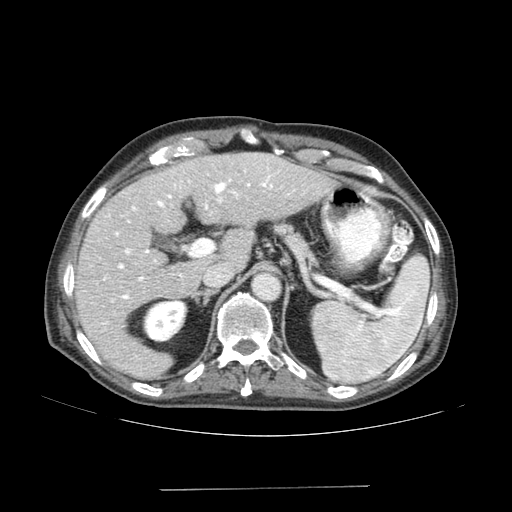
Contrast-enhanced abdominal CT (liver protocol), one axial slice; position 106 of 192 along the scan axis; reconstruction kernel SOFT; 120 kVp; soft-tissue window (W 400 / L 40 HU); 2.5 mm slice thickness; 512 × 512 image matrix. From the clinical record (not read from this slice): diagnosis: hepatocellular carcinoma (patient treated with transarterial chemoembolisation; whether this scan precedes or follows treatment is not stated here); TNM stage (as recorded): Stage-IVA; Child-Pugh class: A; tumour differentiation: poorly differentiated; tumour nodularity: uninodular.
Structures marked on this image (semi-automatically segmented with operator editing):
- liver parenchyma outside the tumour (the mass and vessels are separate outlines, so this box may not span the whole liver): bounding box <74,152,334,378> (left, top, right, bottom; pixels)
- liver vessels: <104,168,273,299>